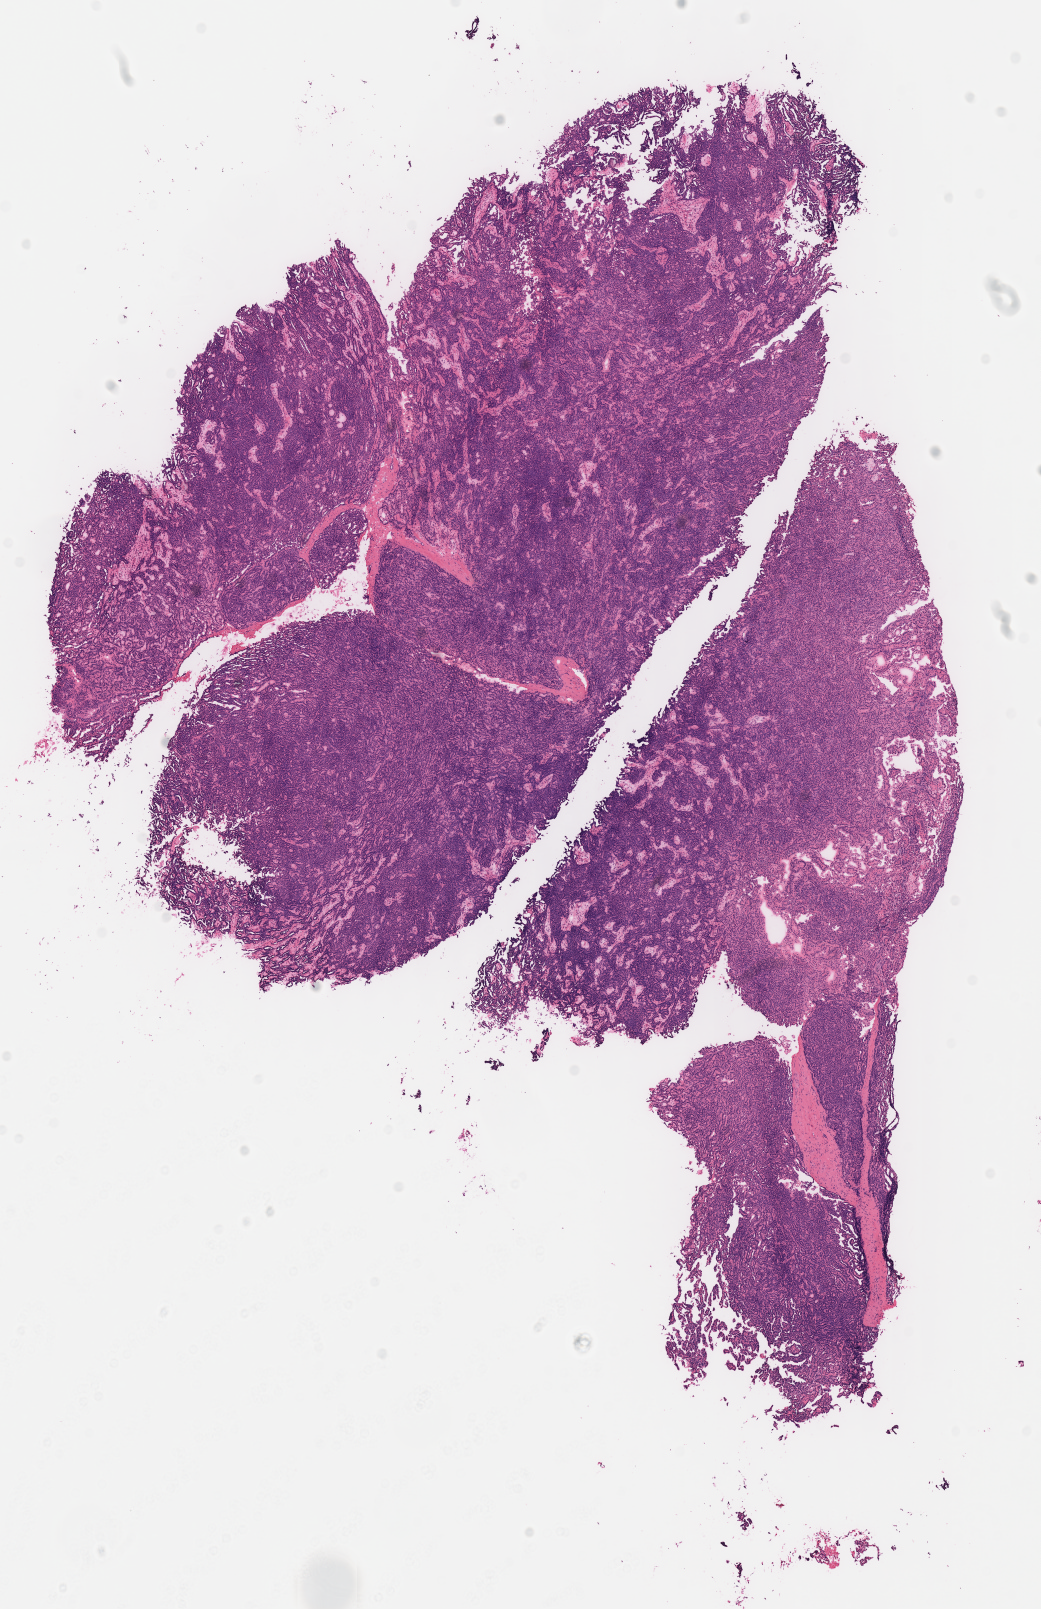
H&E-stained whole-slide image, shown as a low-resolution overview of the whole scanned area (about 8.2 x 12.7 mm); frozen section from the top of the tissue portion; primary tumour sample from the kidney. Patient: male, age at initial diagnosis 52 years. Composition of this section per pathologist review: tumour cells 95%, tumour nuclei 95%, normal cells 0%, stromal cells 5%, necrosis 0%.
AJCC pathologic stage: I. Diagnosis: Papillary adenocarcinoma, NOS.